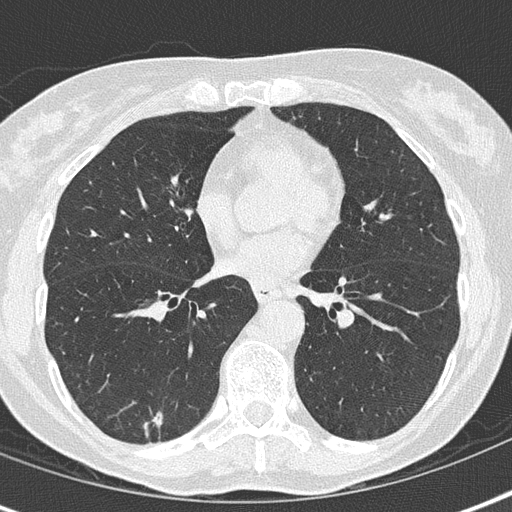
Axial slice from a low-dose chest CT screening exam; first (baseline) screen; lung window (W 1500 / L -600 HU); lung (sharp) reconstruction kernel (B50f); 120 kVp; slice 90 of 155 in the series. Female, age 69 years at enrolment.
Expert-annotated lung lesion, bounding box [x1, y1, x2, y2] px = [119, 390, 182, 449]. The screening reader recorded 2 non-calcified nodules or masses ≥4 mm on this exam (right lower lobe, left lower lobe); which of them this box marks is not recorded. Official screen result: positive, change unspecified: nodule(s) >= 4 mm or enlarging nodule(s), mass(es), or other non-specific abnormalities suspicious for lung cancer. Participant outcome: lung cancer diagnosed 476 days after this screen (after the second annual screen) — adenocarcinoma, NOS, right lower lobe, moderately differentiated (G2), stage IA (AJCC 6th edition), 16 mm at pathology.